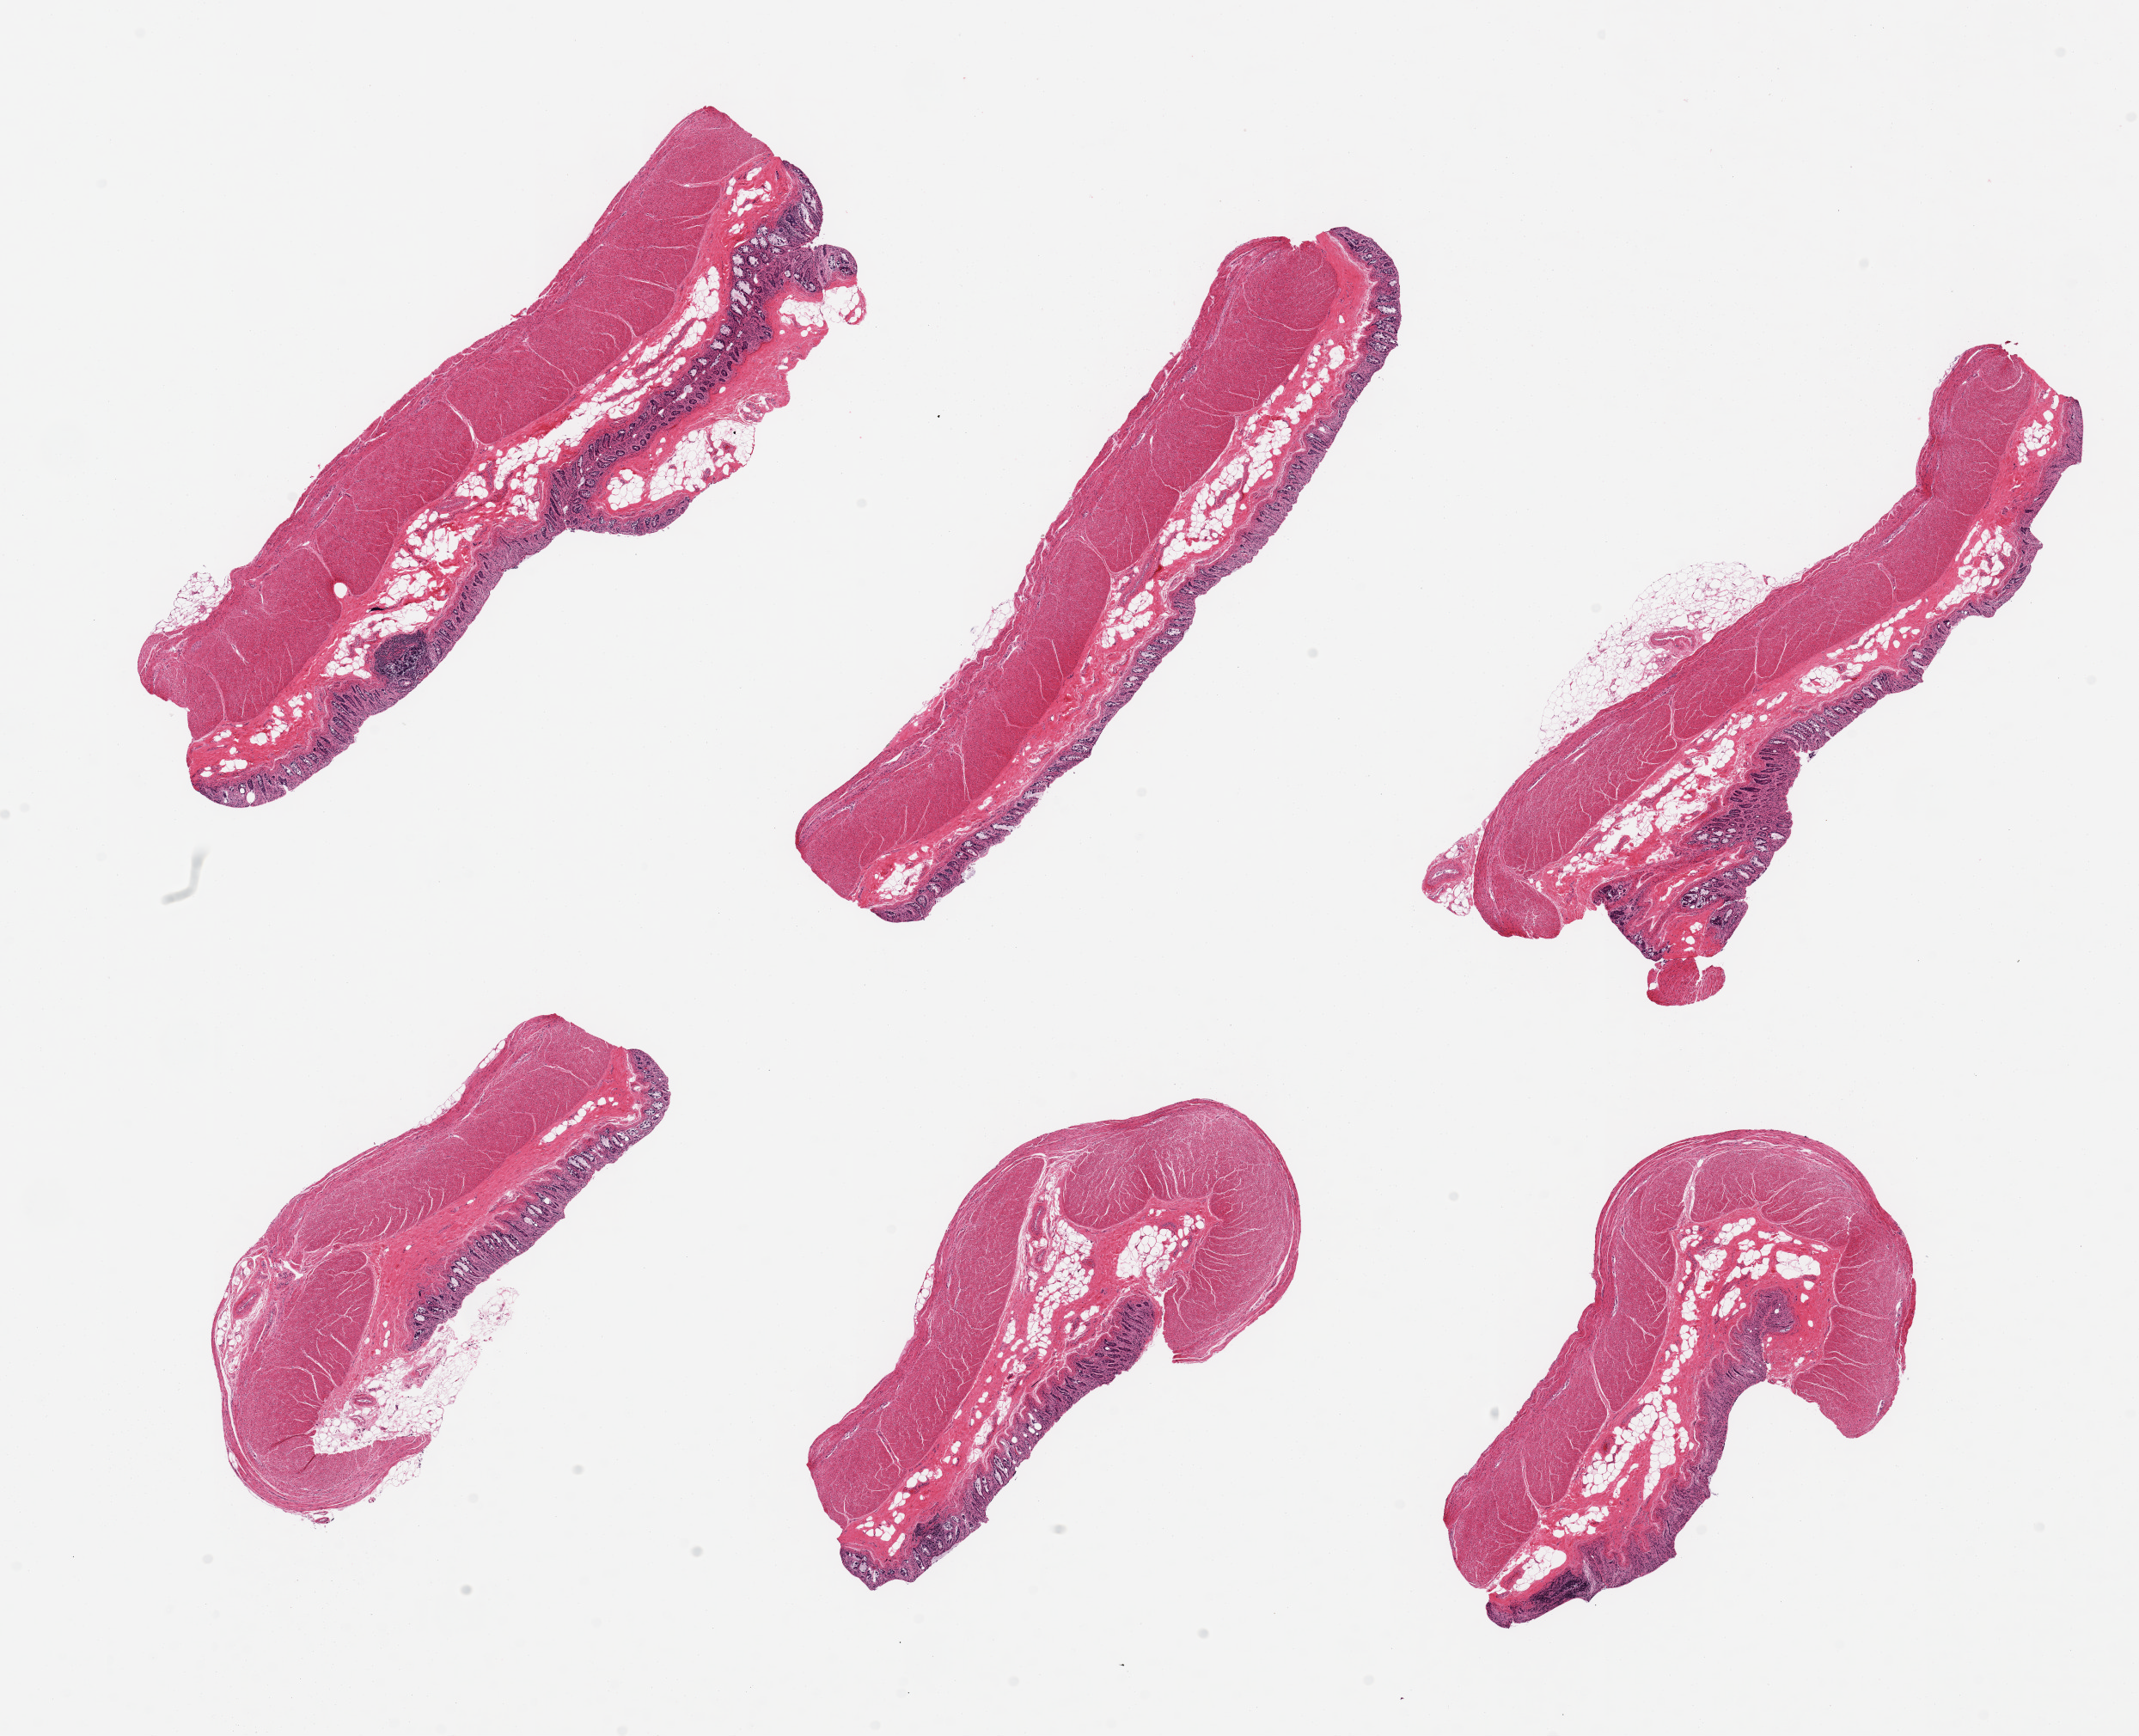
Digitized hematoxylin and eosin (H&E)-stained section, low-resolution overview of the scanned area, about 19.7 x 16.0 mm, PAXgene-fixed paraffin-embedded (PFPE) section, target tissue: sigmoid colon, donor tissue sample.
* pathologist's review note for this sample: 6 pieces, confirmed target muscularis; ~15-20% 'contaminant' mucosa present